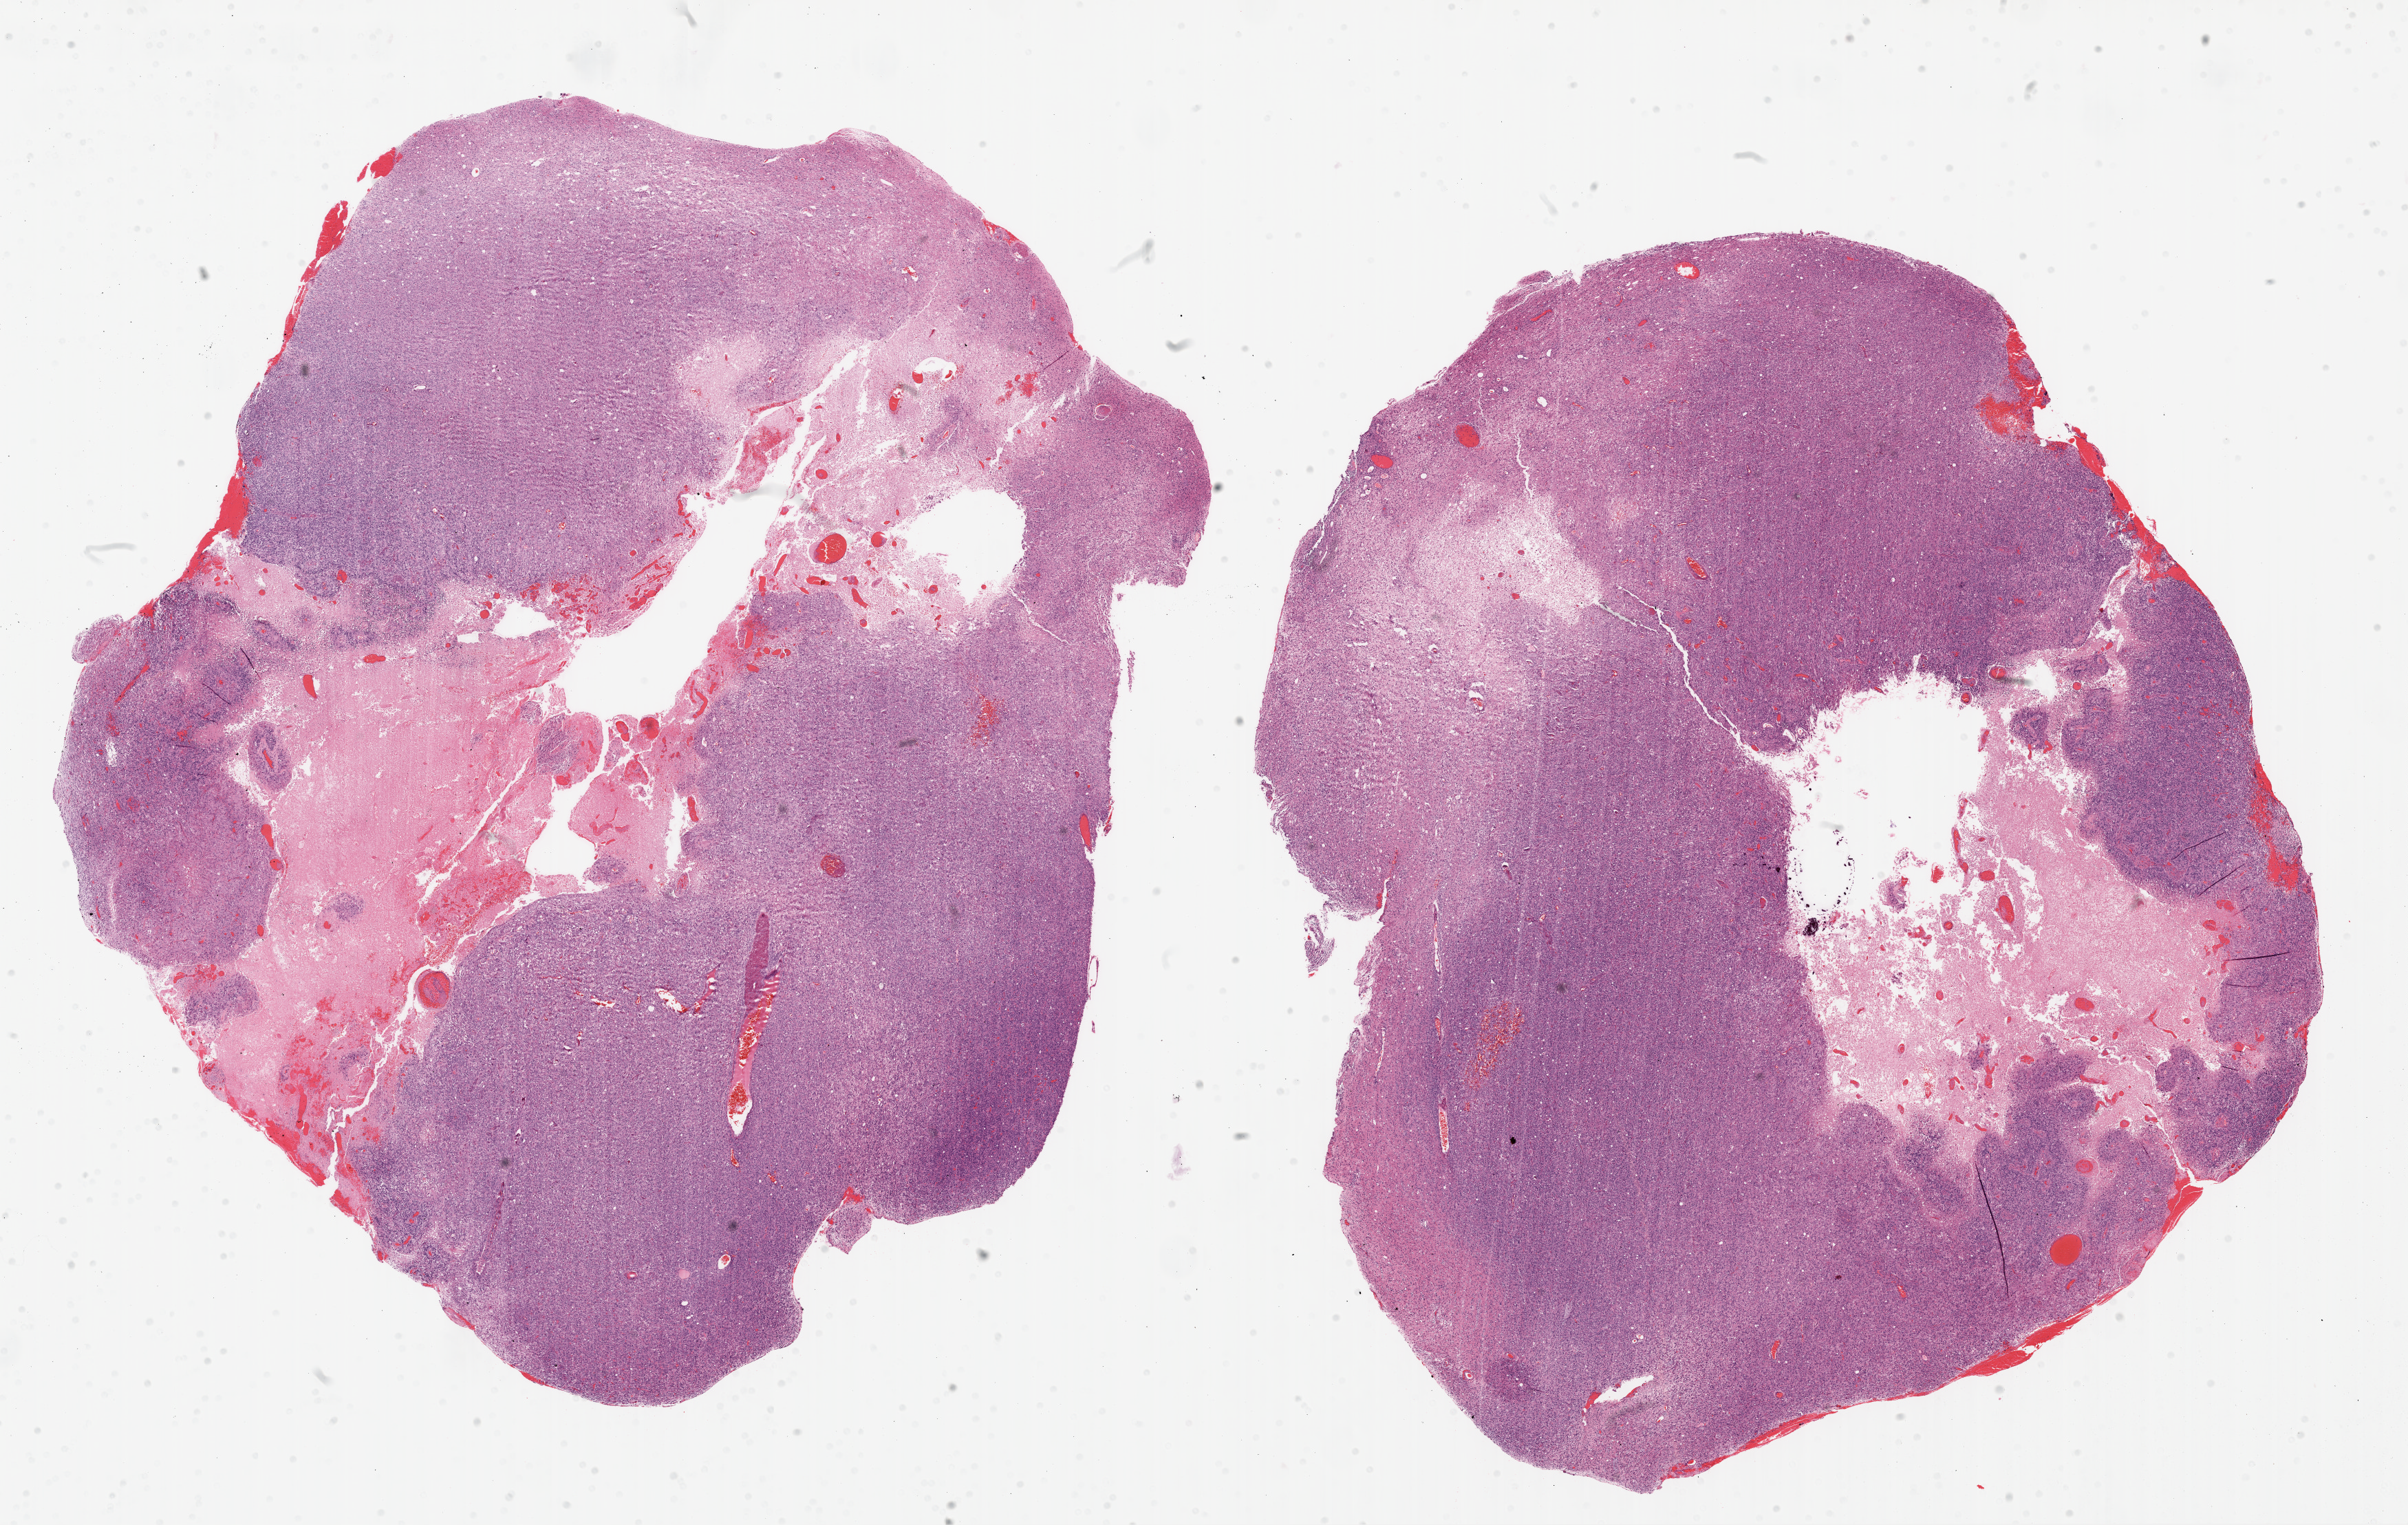
Whole-slide histology image, Hematoxylin and eosin (H&E) stained, whole scanned area (about 28.1 x 17.8 mm) shown as a low-resolution overview, formalin-fixed paraffin-embedded (FFPE) diagnostic section, brain, primary tumour sample. Patient: female, age at initial diagnosis 34 years.
Pathologic diagnosis: Glioblastoma.